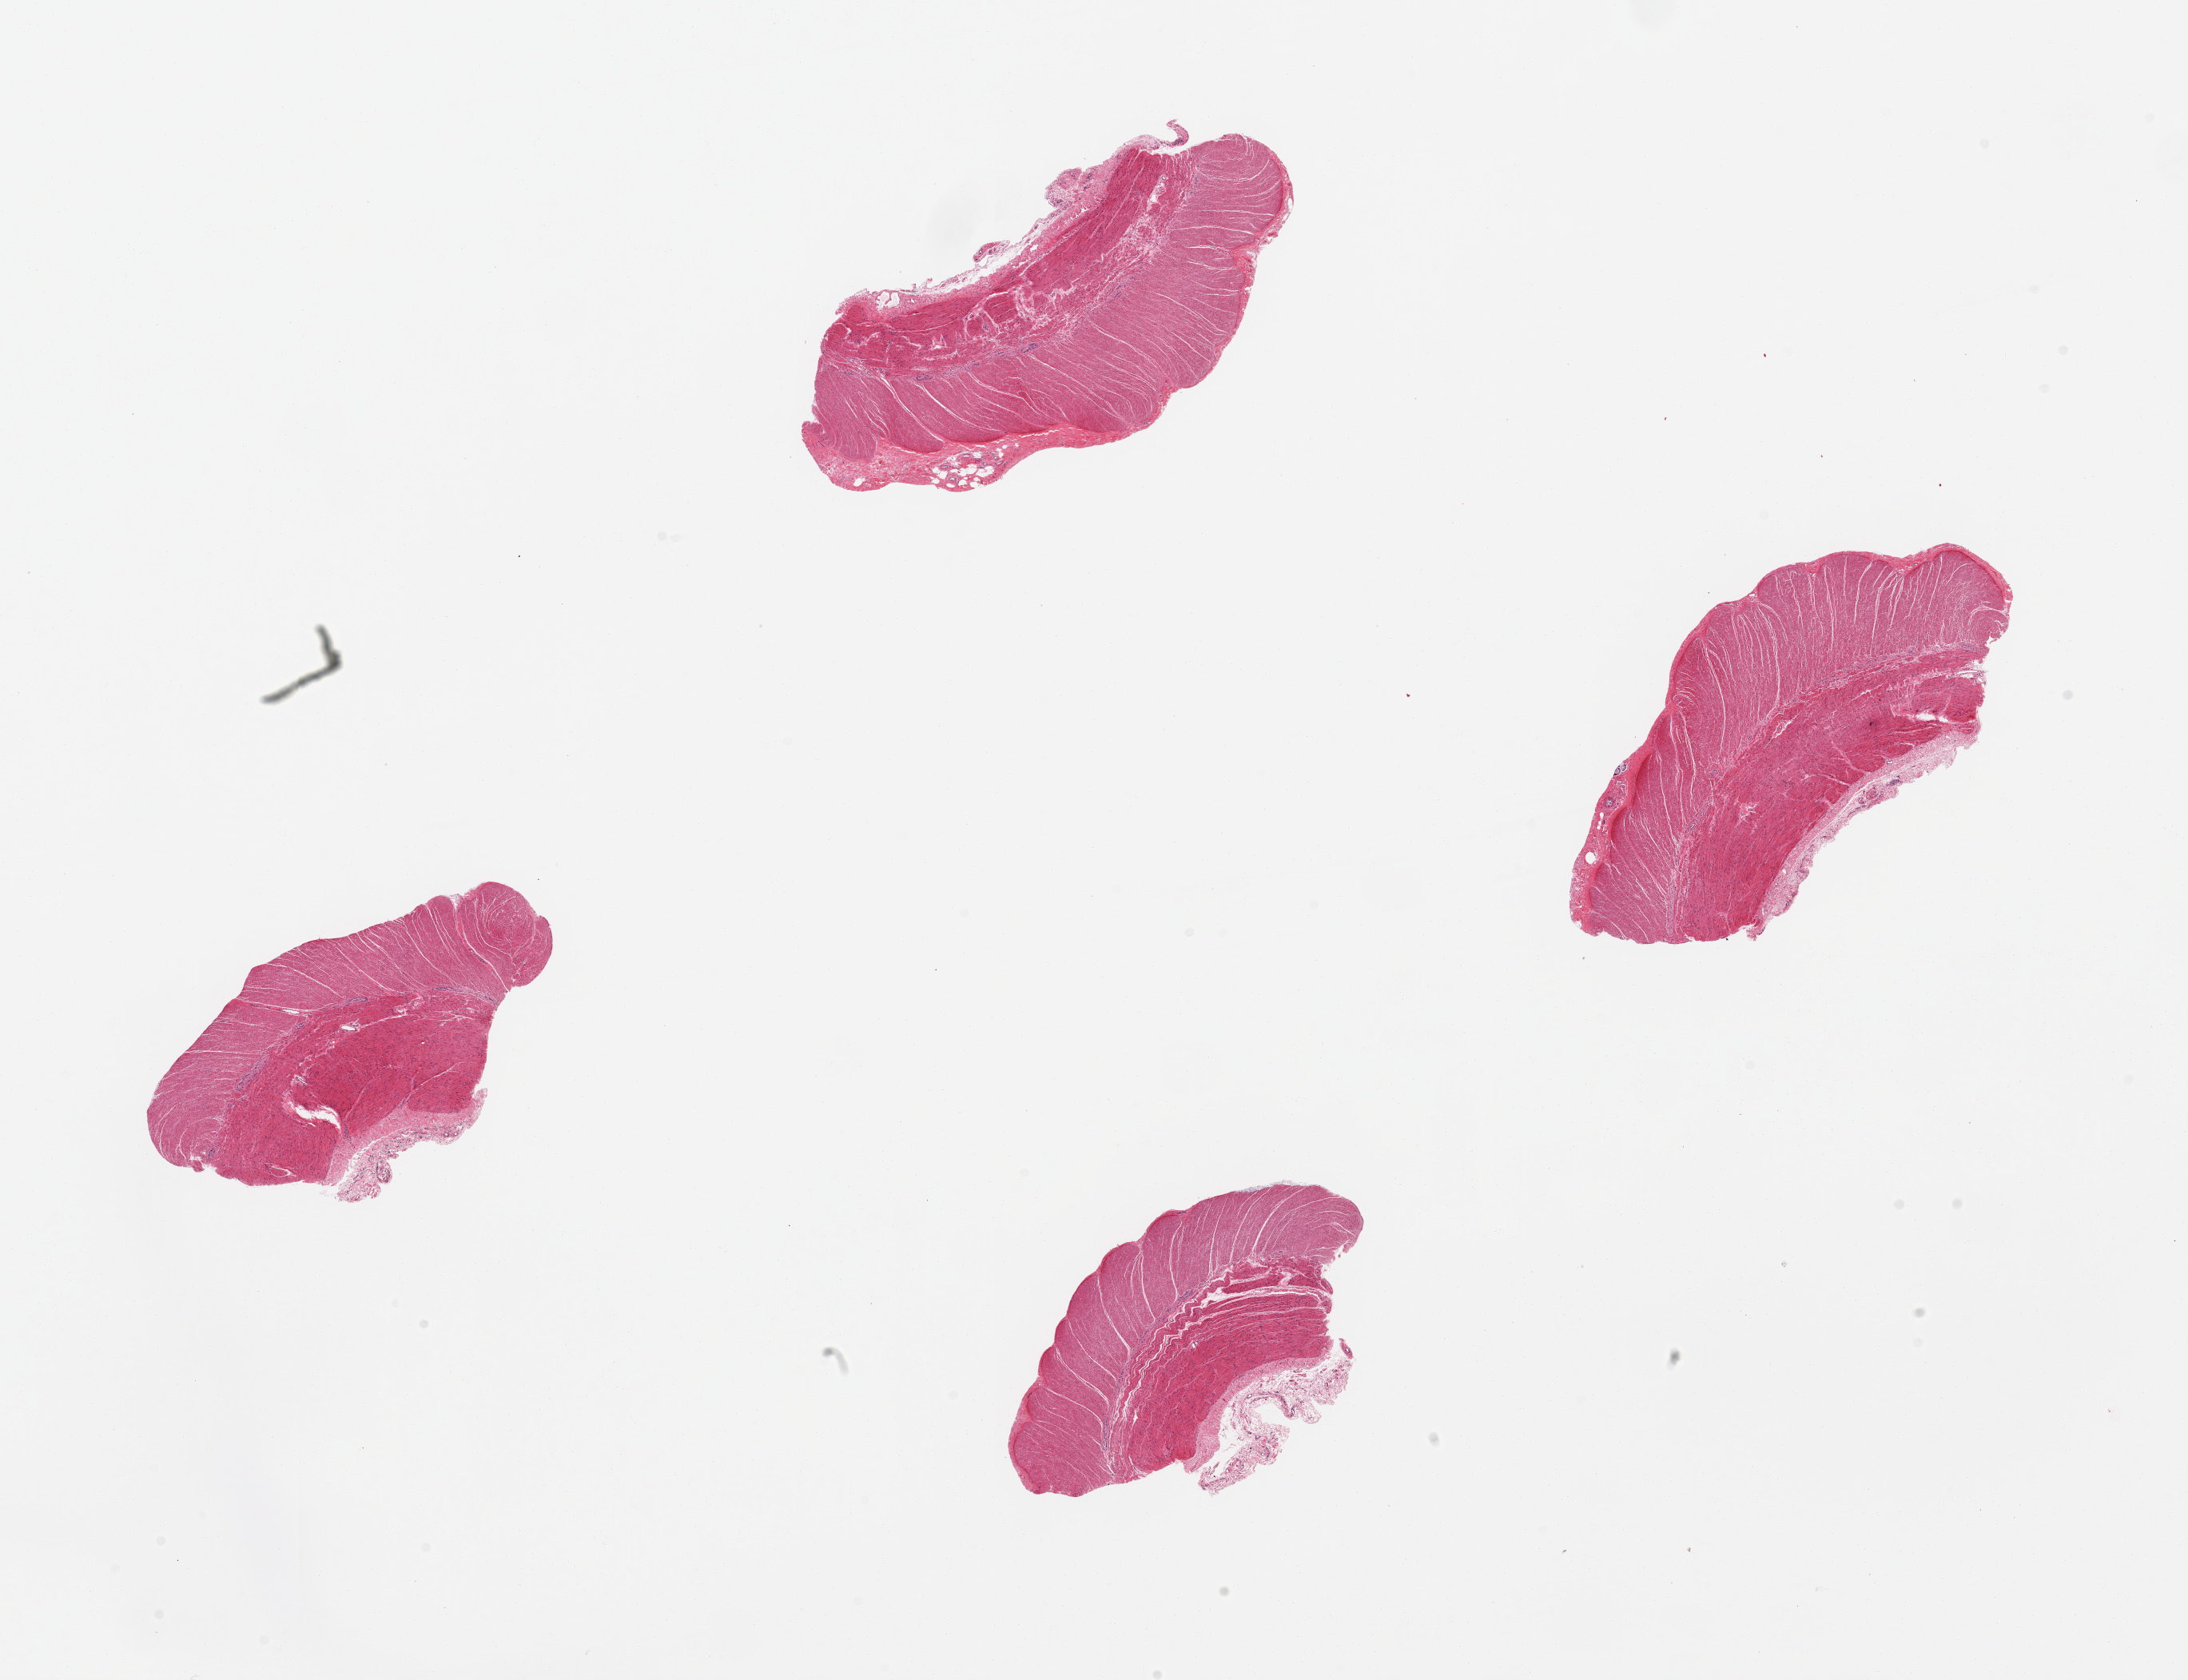
Whole-slide image, hematoxylin and eosin (H&E) stain, shown as a low-resolution overview of the whole scanned area (about 21.7 x 16.6 mm, slide scanned at 20x); PAXgene-fixed, paraffin-embedded tissue; sampled site (target tissue): sigmoid colon; donor tissue sample.
Review note (as recorded): 4 pieces; well trimmed.